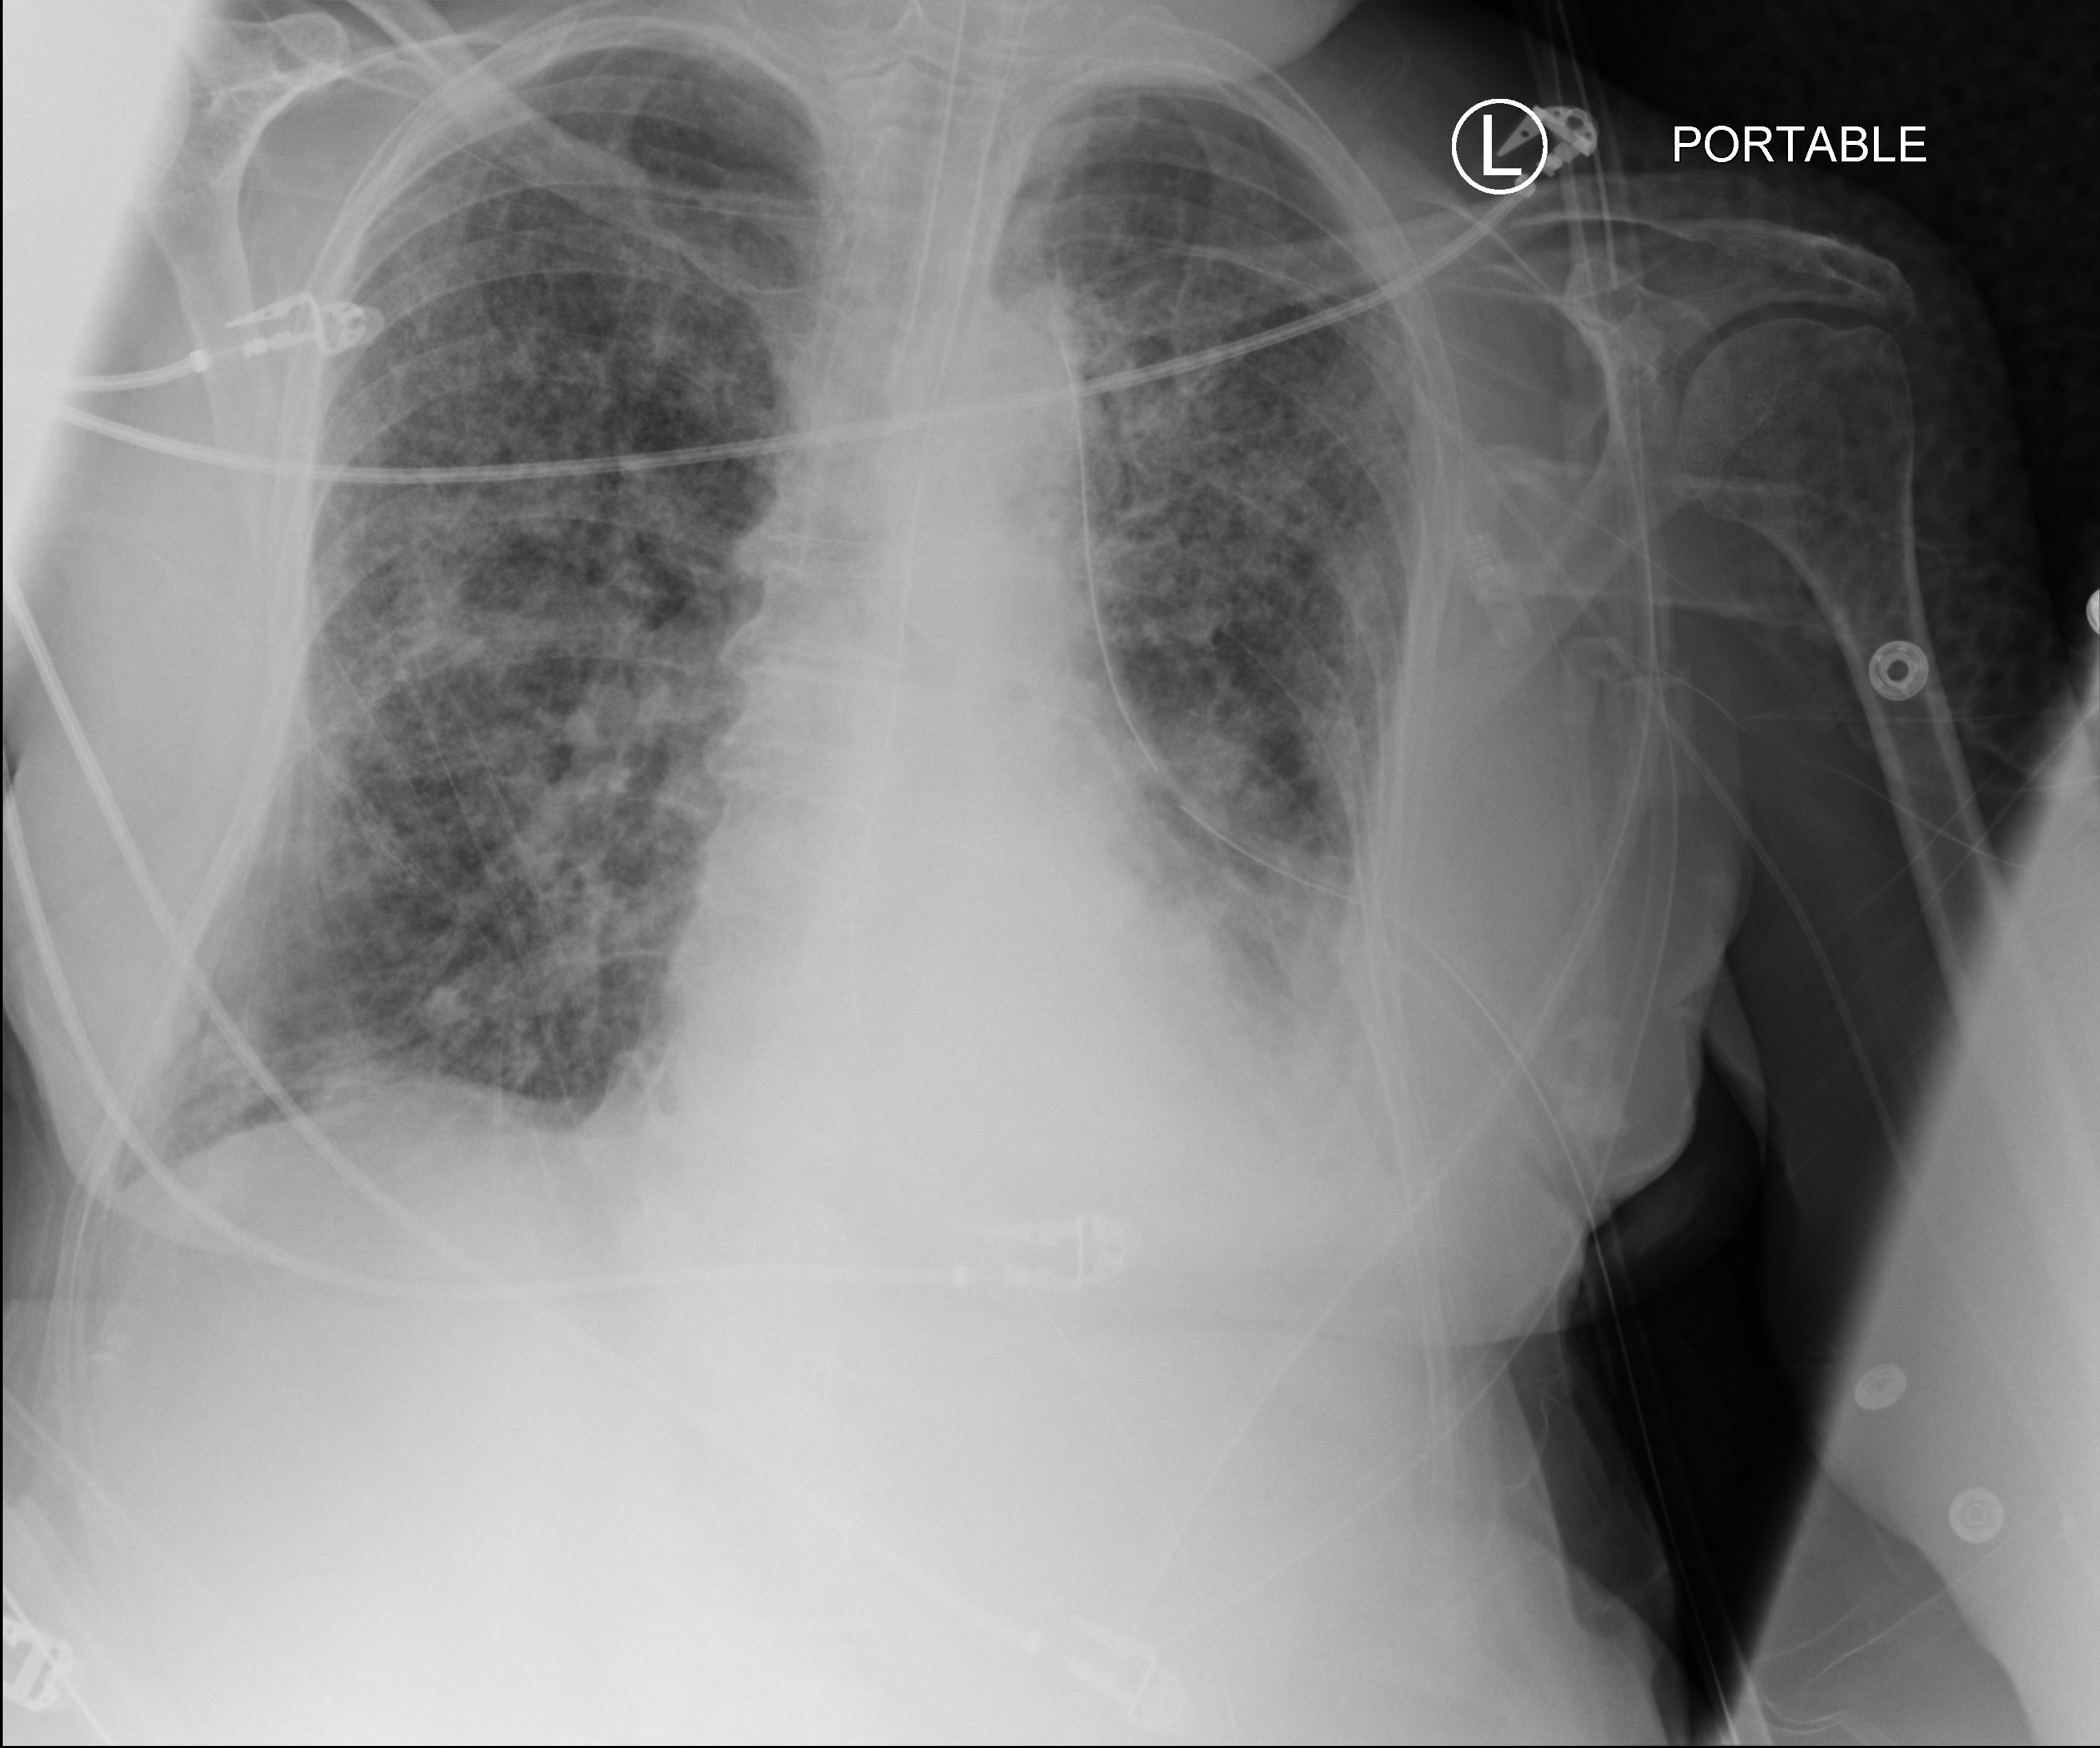
Portable chest radiograph; anteroposterior (AP) projection. Patient hospitalised with COVID-19; female, aged 75–90 years.
Admission-level facts for this patient (not findings on this image; timing relative to this image not recorded): length of hospital stay: 70 days; mechanically ventilated during this hospital stay: yes; admitted to intensive care during this hospital stay: yes.